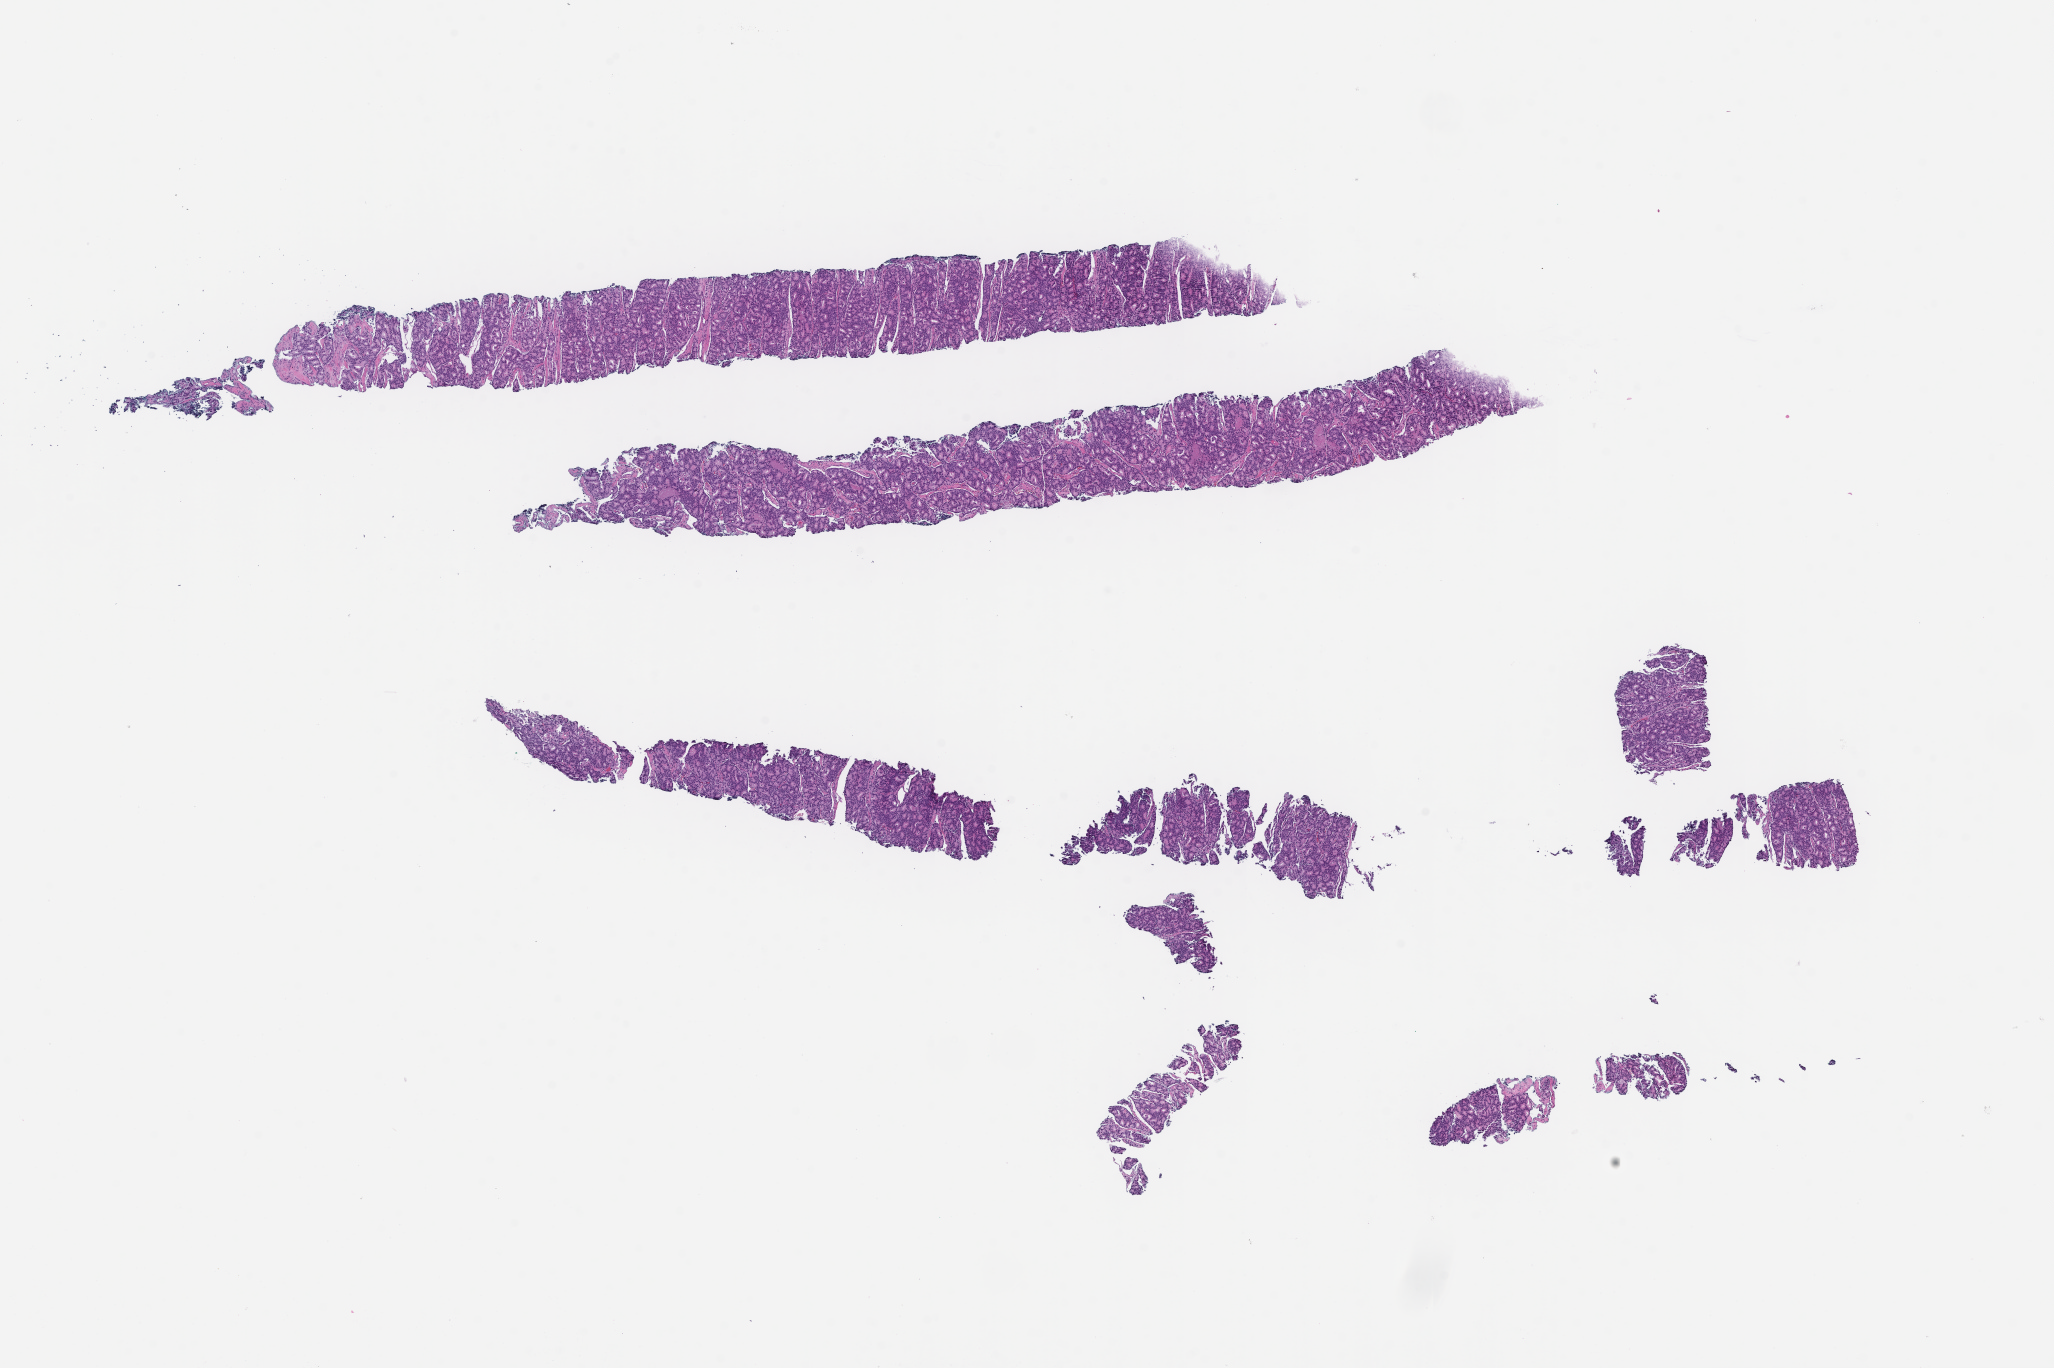
Digitized haematoxylin and eosin-stained section, whole scanned area (about 16.6 x 11.0 mm) shown as a low-resolution overview, formalin-fixed, paraffin-embedded (FFPE) tissue, archival tissue. Patient: male.
This section: metastasis (sampled organ not recorded). Patient diagnosis (primary): Prostate Carcinoma.